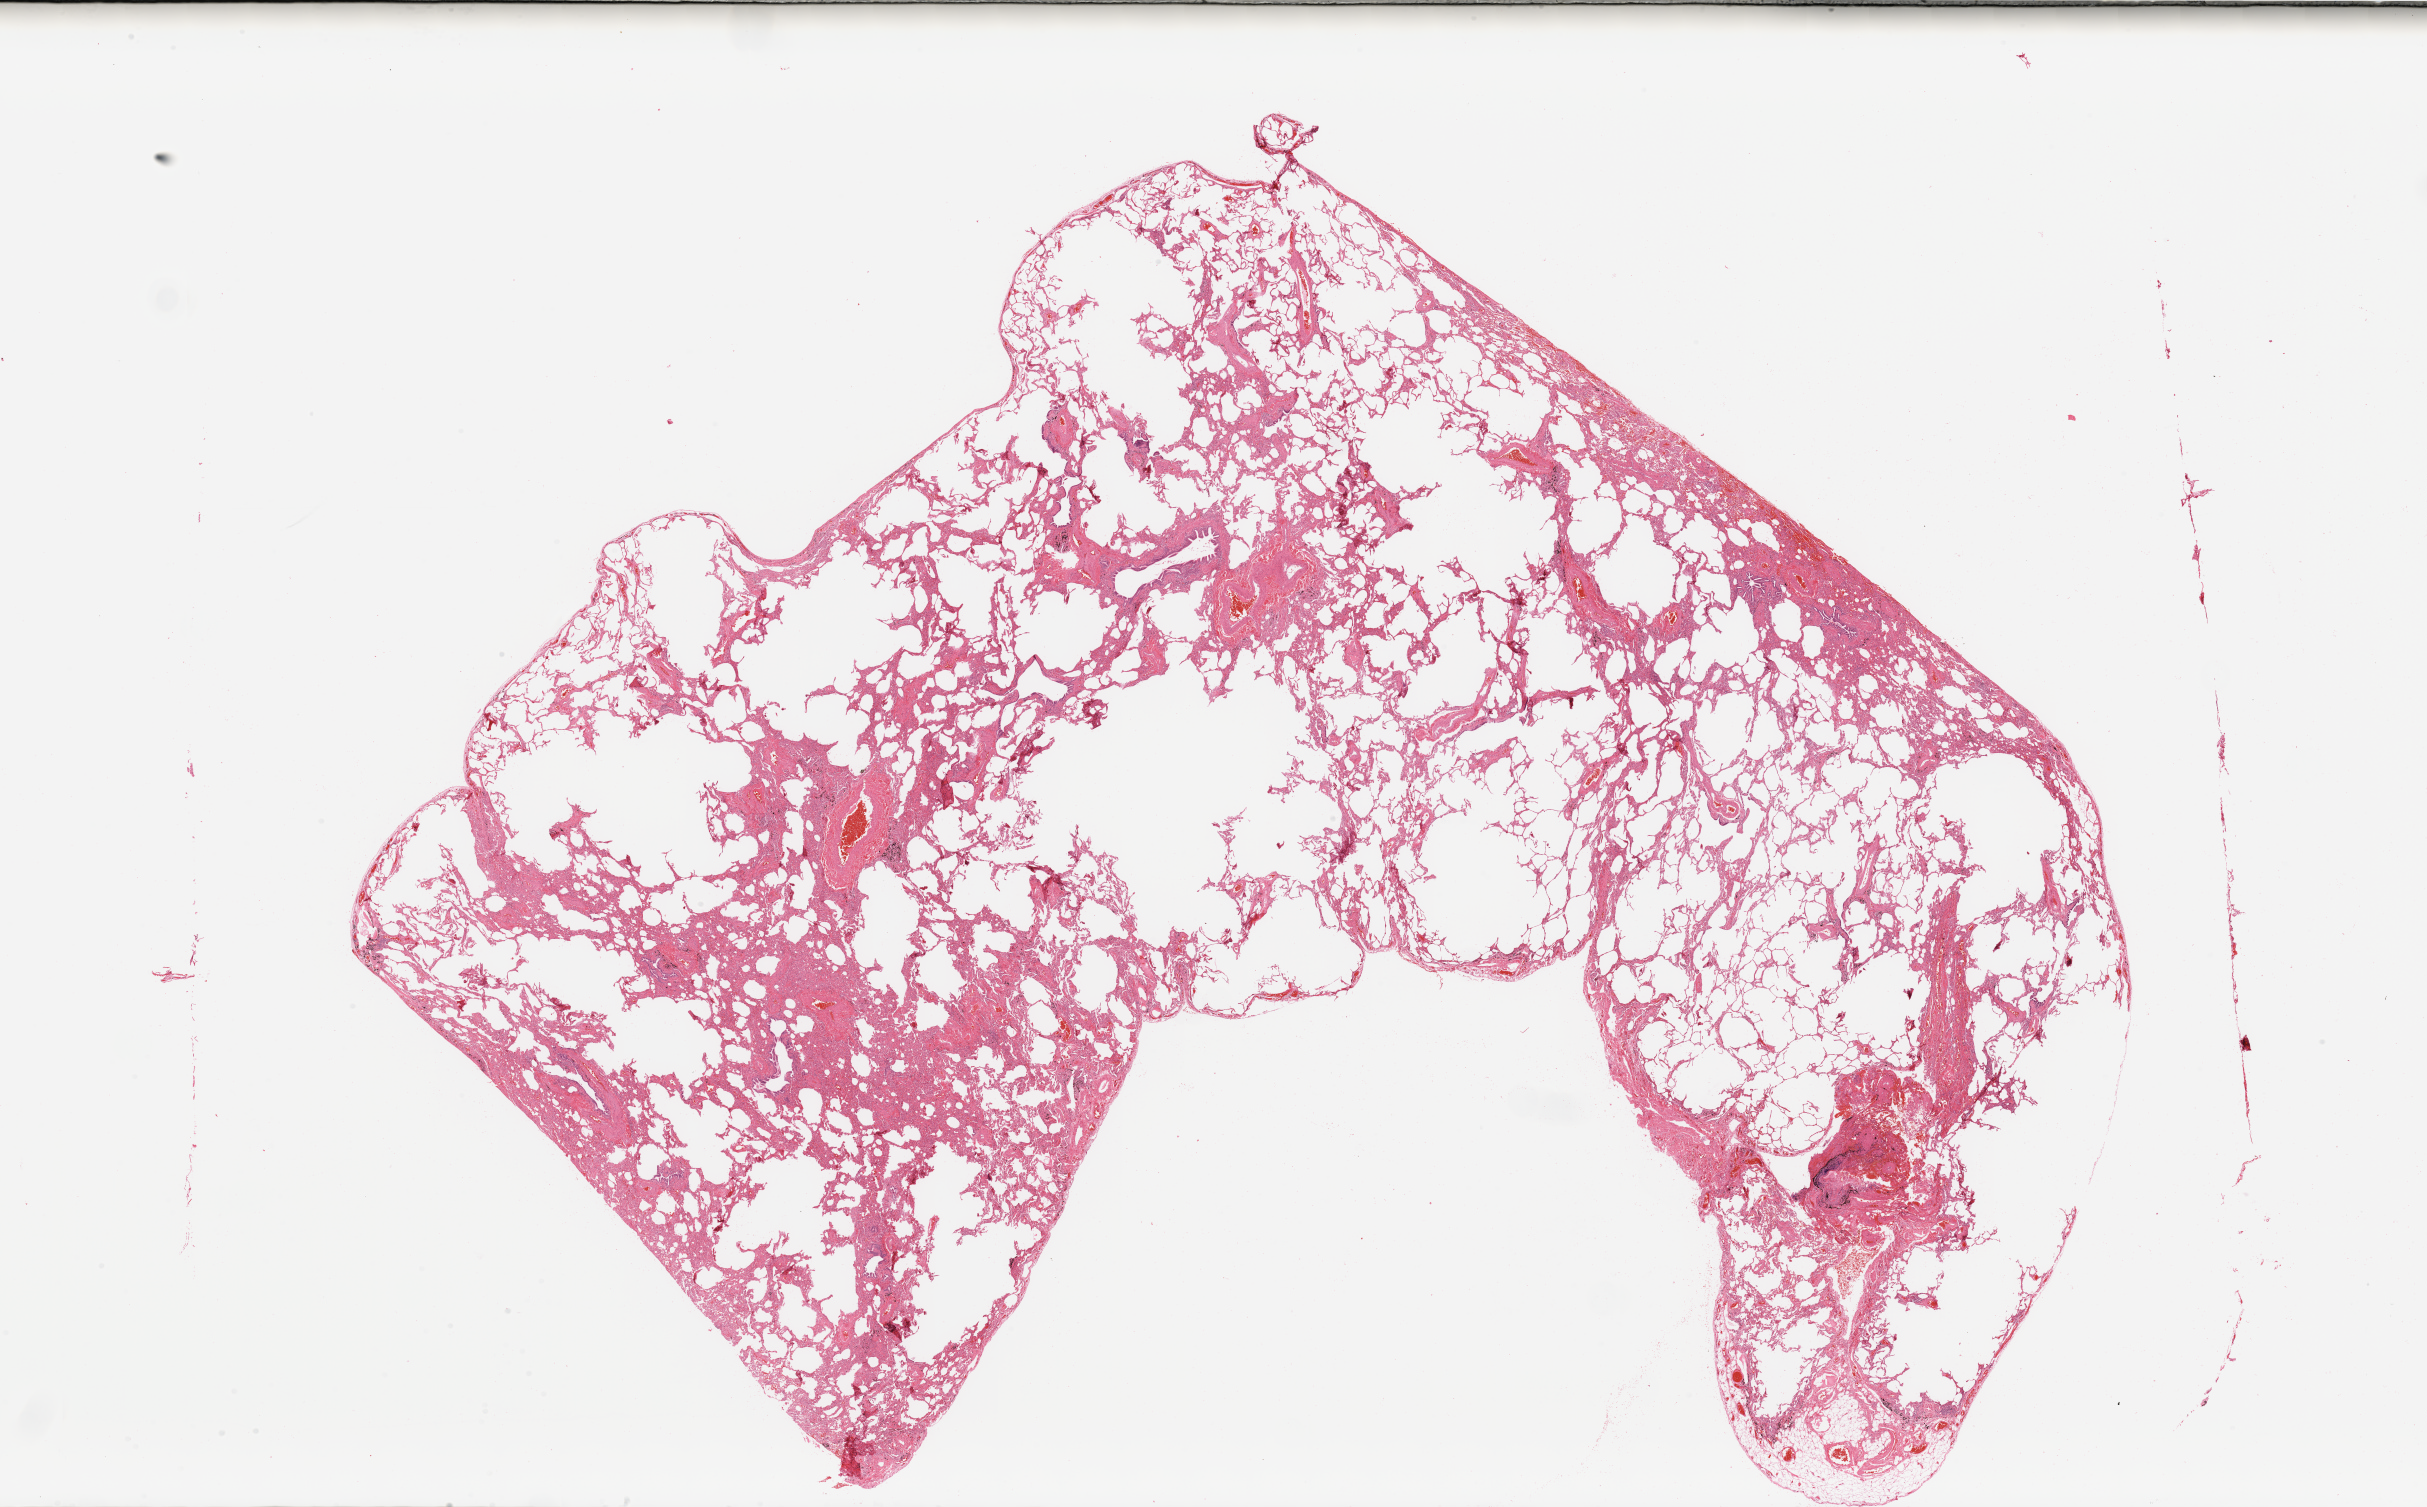
H&E-stained whole-slide image, a low-resolution overview of the entire scanned area, about 38.4 x 23.8 mm (slide scanned at 20x); lung, tissue type not recorded.
Patient diagnosis (cohort enrolment): lung adenocarcinoma (lung).